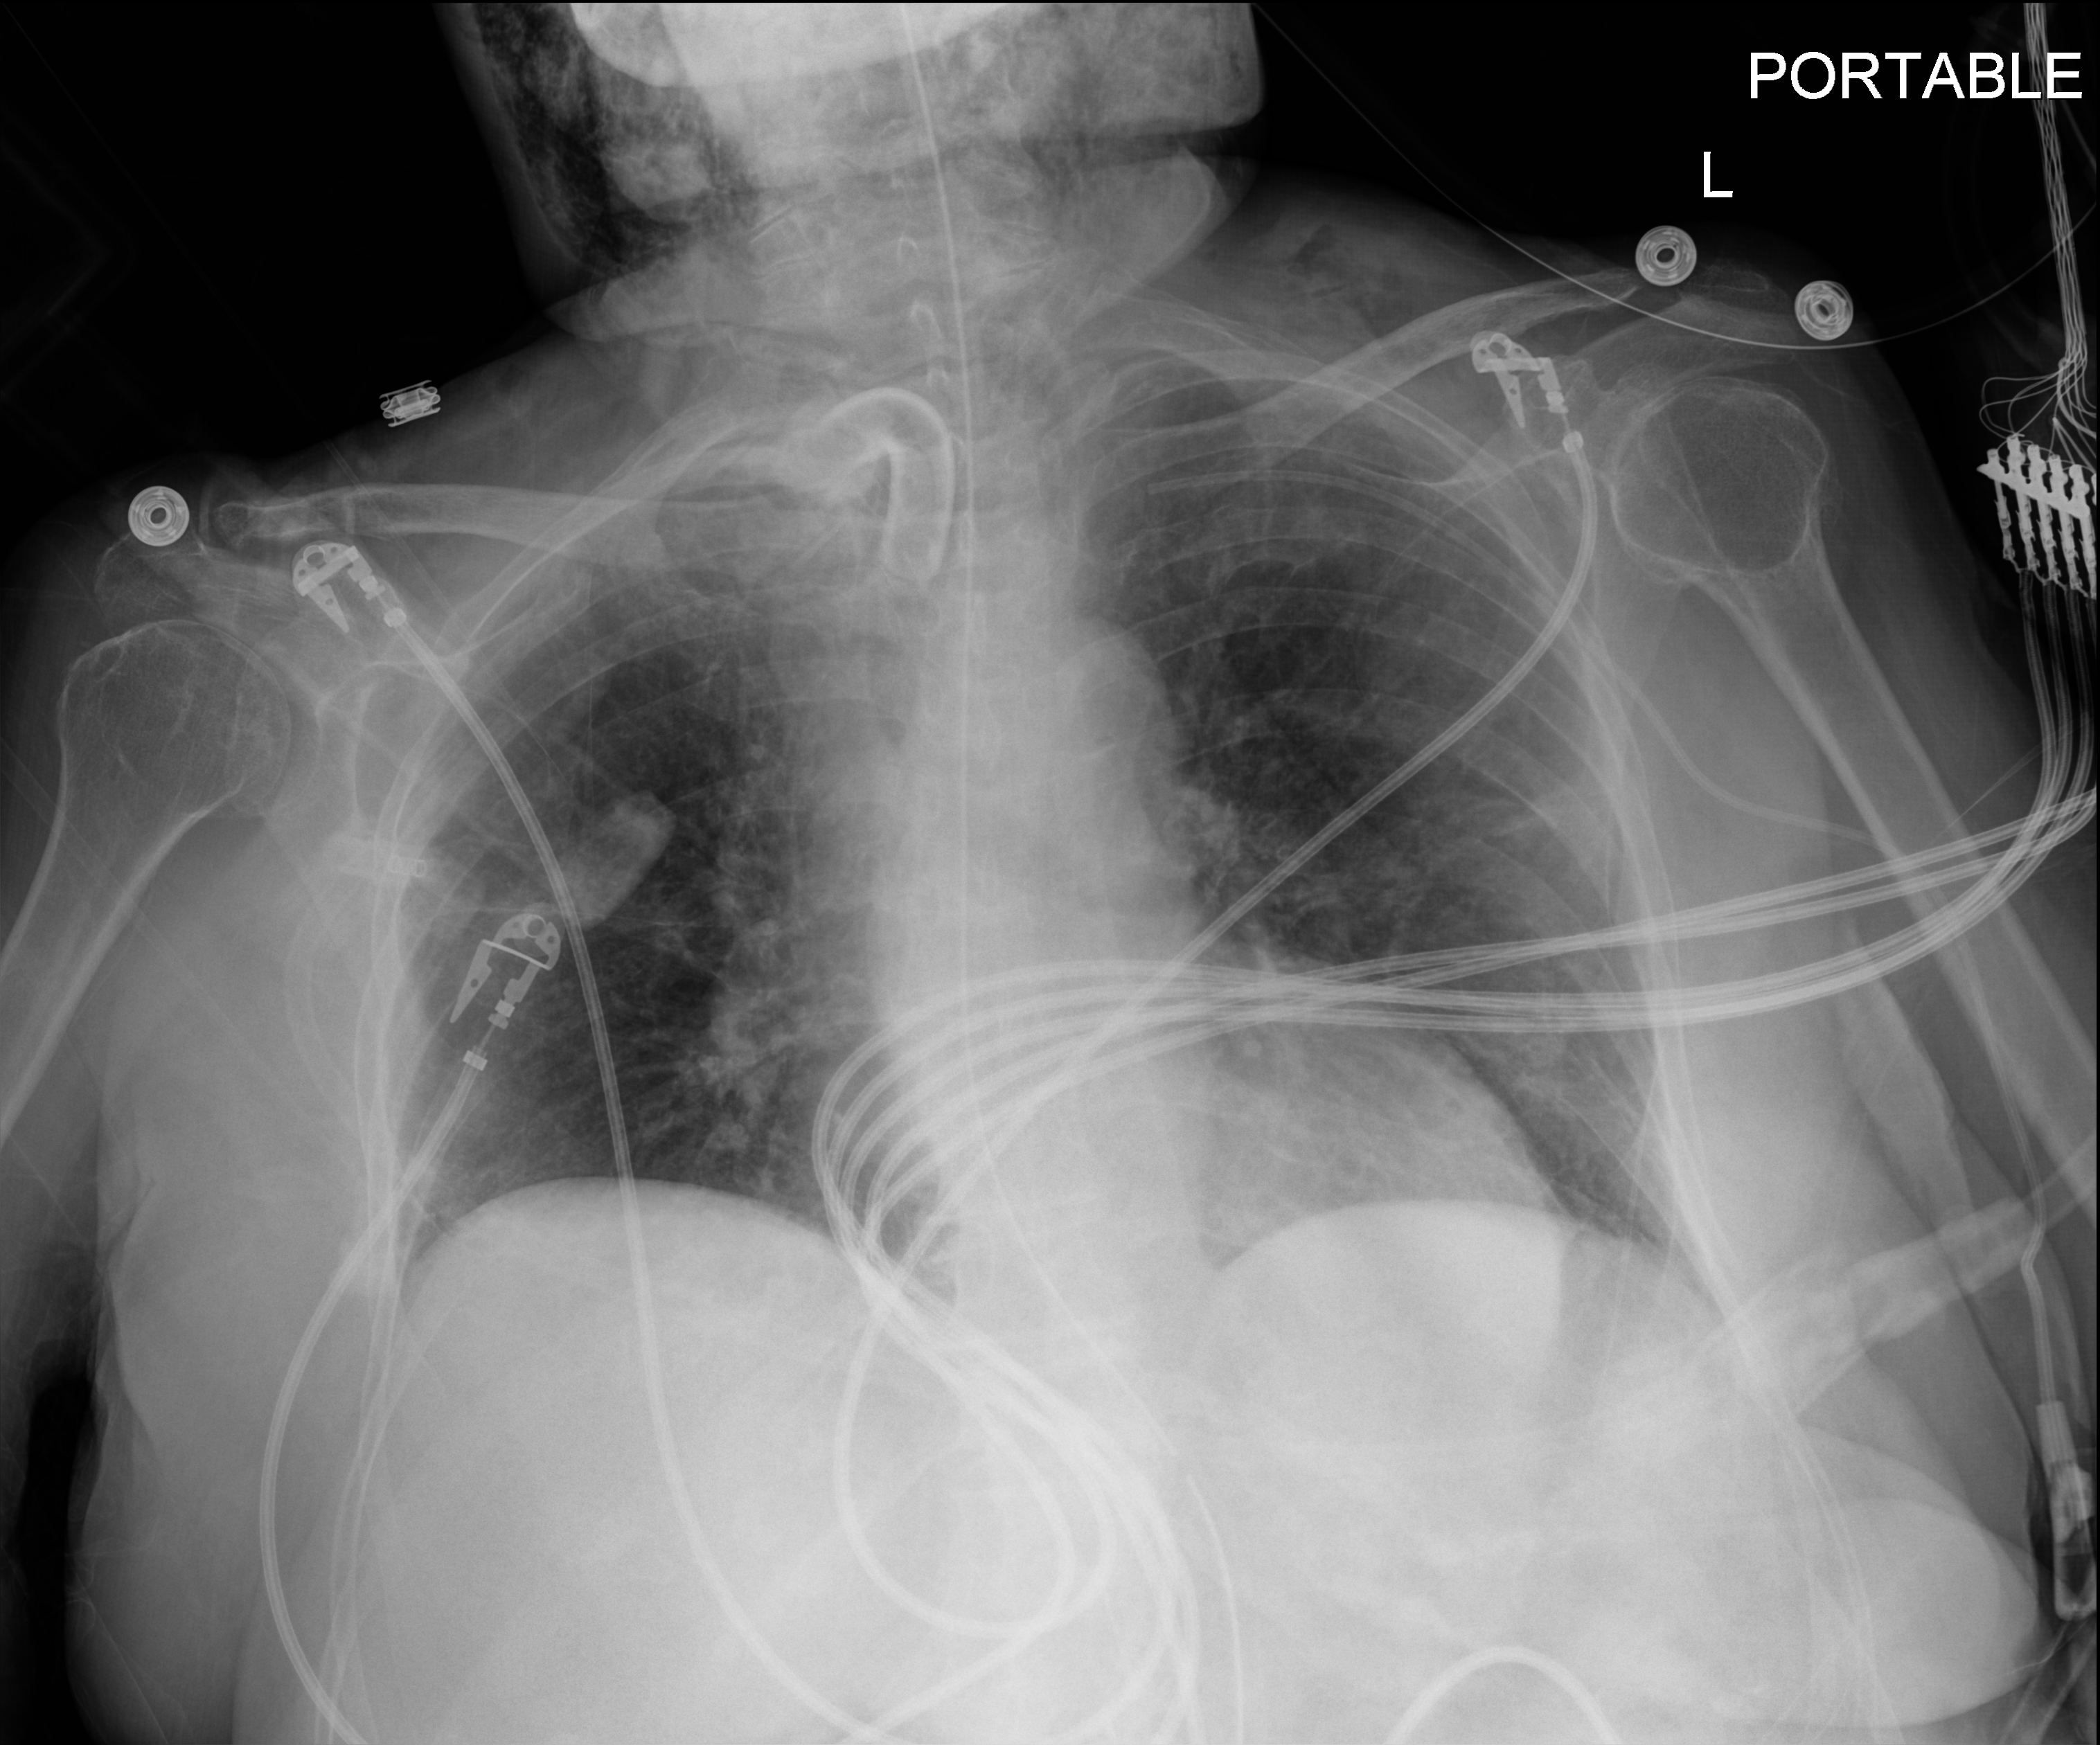
Chest X-ray (portable); anteroposterior (AP) projection. Patient hospitalised with COVID-19; female, aged 75–90 years.
Hospital-stay facts (about this admission, not read from this image; timing relative to this image not recorded): mechanically ventilated during this hospital stay: yes; admitted to intensive care during this hospital stay: yes.